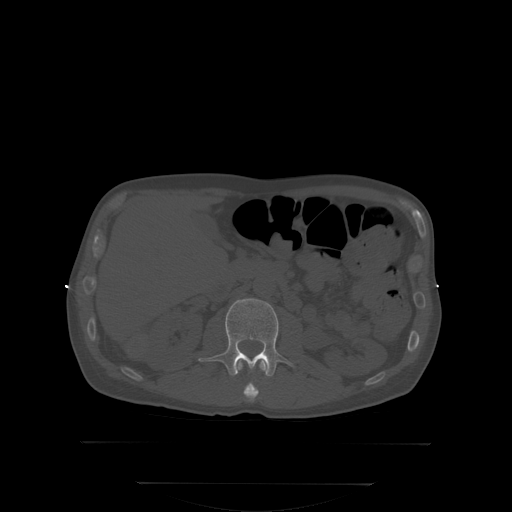
CT including the spine, one axial slice; position 141 of 350 along the scan axis; bone window (W 1800 / L 400 HU); 512 × 512 image matrix, field of view 500 × 500 mm. Male patient, age 58 years. Case-level facts recorded for this patient, not image findings: primary cancer: prostate.
Outlined on this slice (semi-automatically segmented with operator editing):
- L1 vertebra: bounding box (x1, y1, x2, y2) in pixels: (239, 361, 266, 402)
- L2 vertebra: (200, 298, 296, 377)